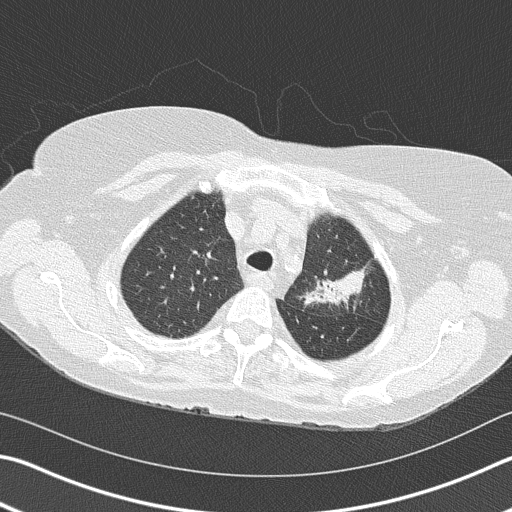
Low-dose screening chest CT, axial slice; second annual screen; lung window (W 1500 / L -600 HU); 2 mm slice thickness; 512 × 512 image matrix. Female participant, aged 68 years at enrolment. Former smoker at enrolment.
Expert-annotated lung lesion, bounding box [x1, y1, x2, y2] px = [291, 228, 377, 322]. Screening reader's record for this exam (one nodule recorded; not confirmed to be the boxed lesion): non-calcified nodule or mass ≥4 mm, left upper lobe, 4 × 2 mm, spiculated (stellate) margins, soft tissue attenuation, pre-existing on the prior screen: yes; interval growth: yes. Official screen result: positive, other. Lung cancer was diagnosed 392 days after this screen (after the third annual screen): adenocarcinoma, NOS, left upper lobe, poorly differentiated (G3), stage IB (AJCC 6th edition), 50 mm at pathology.